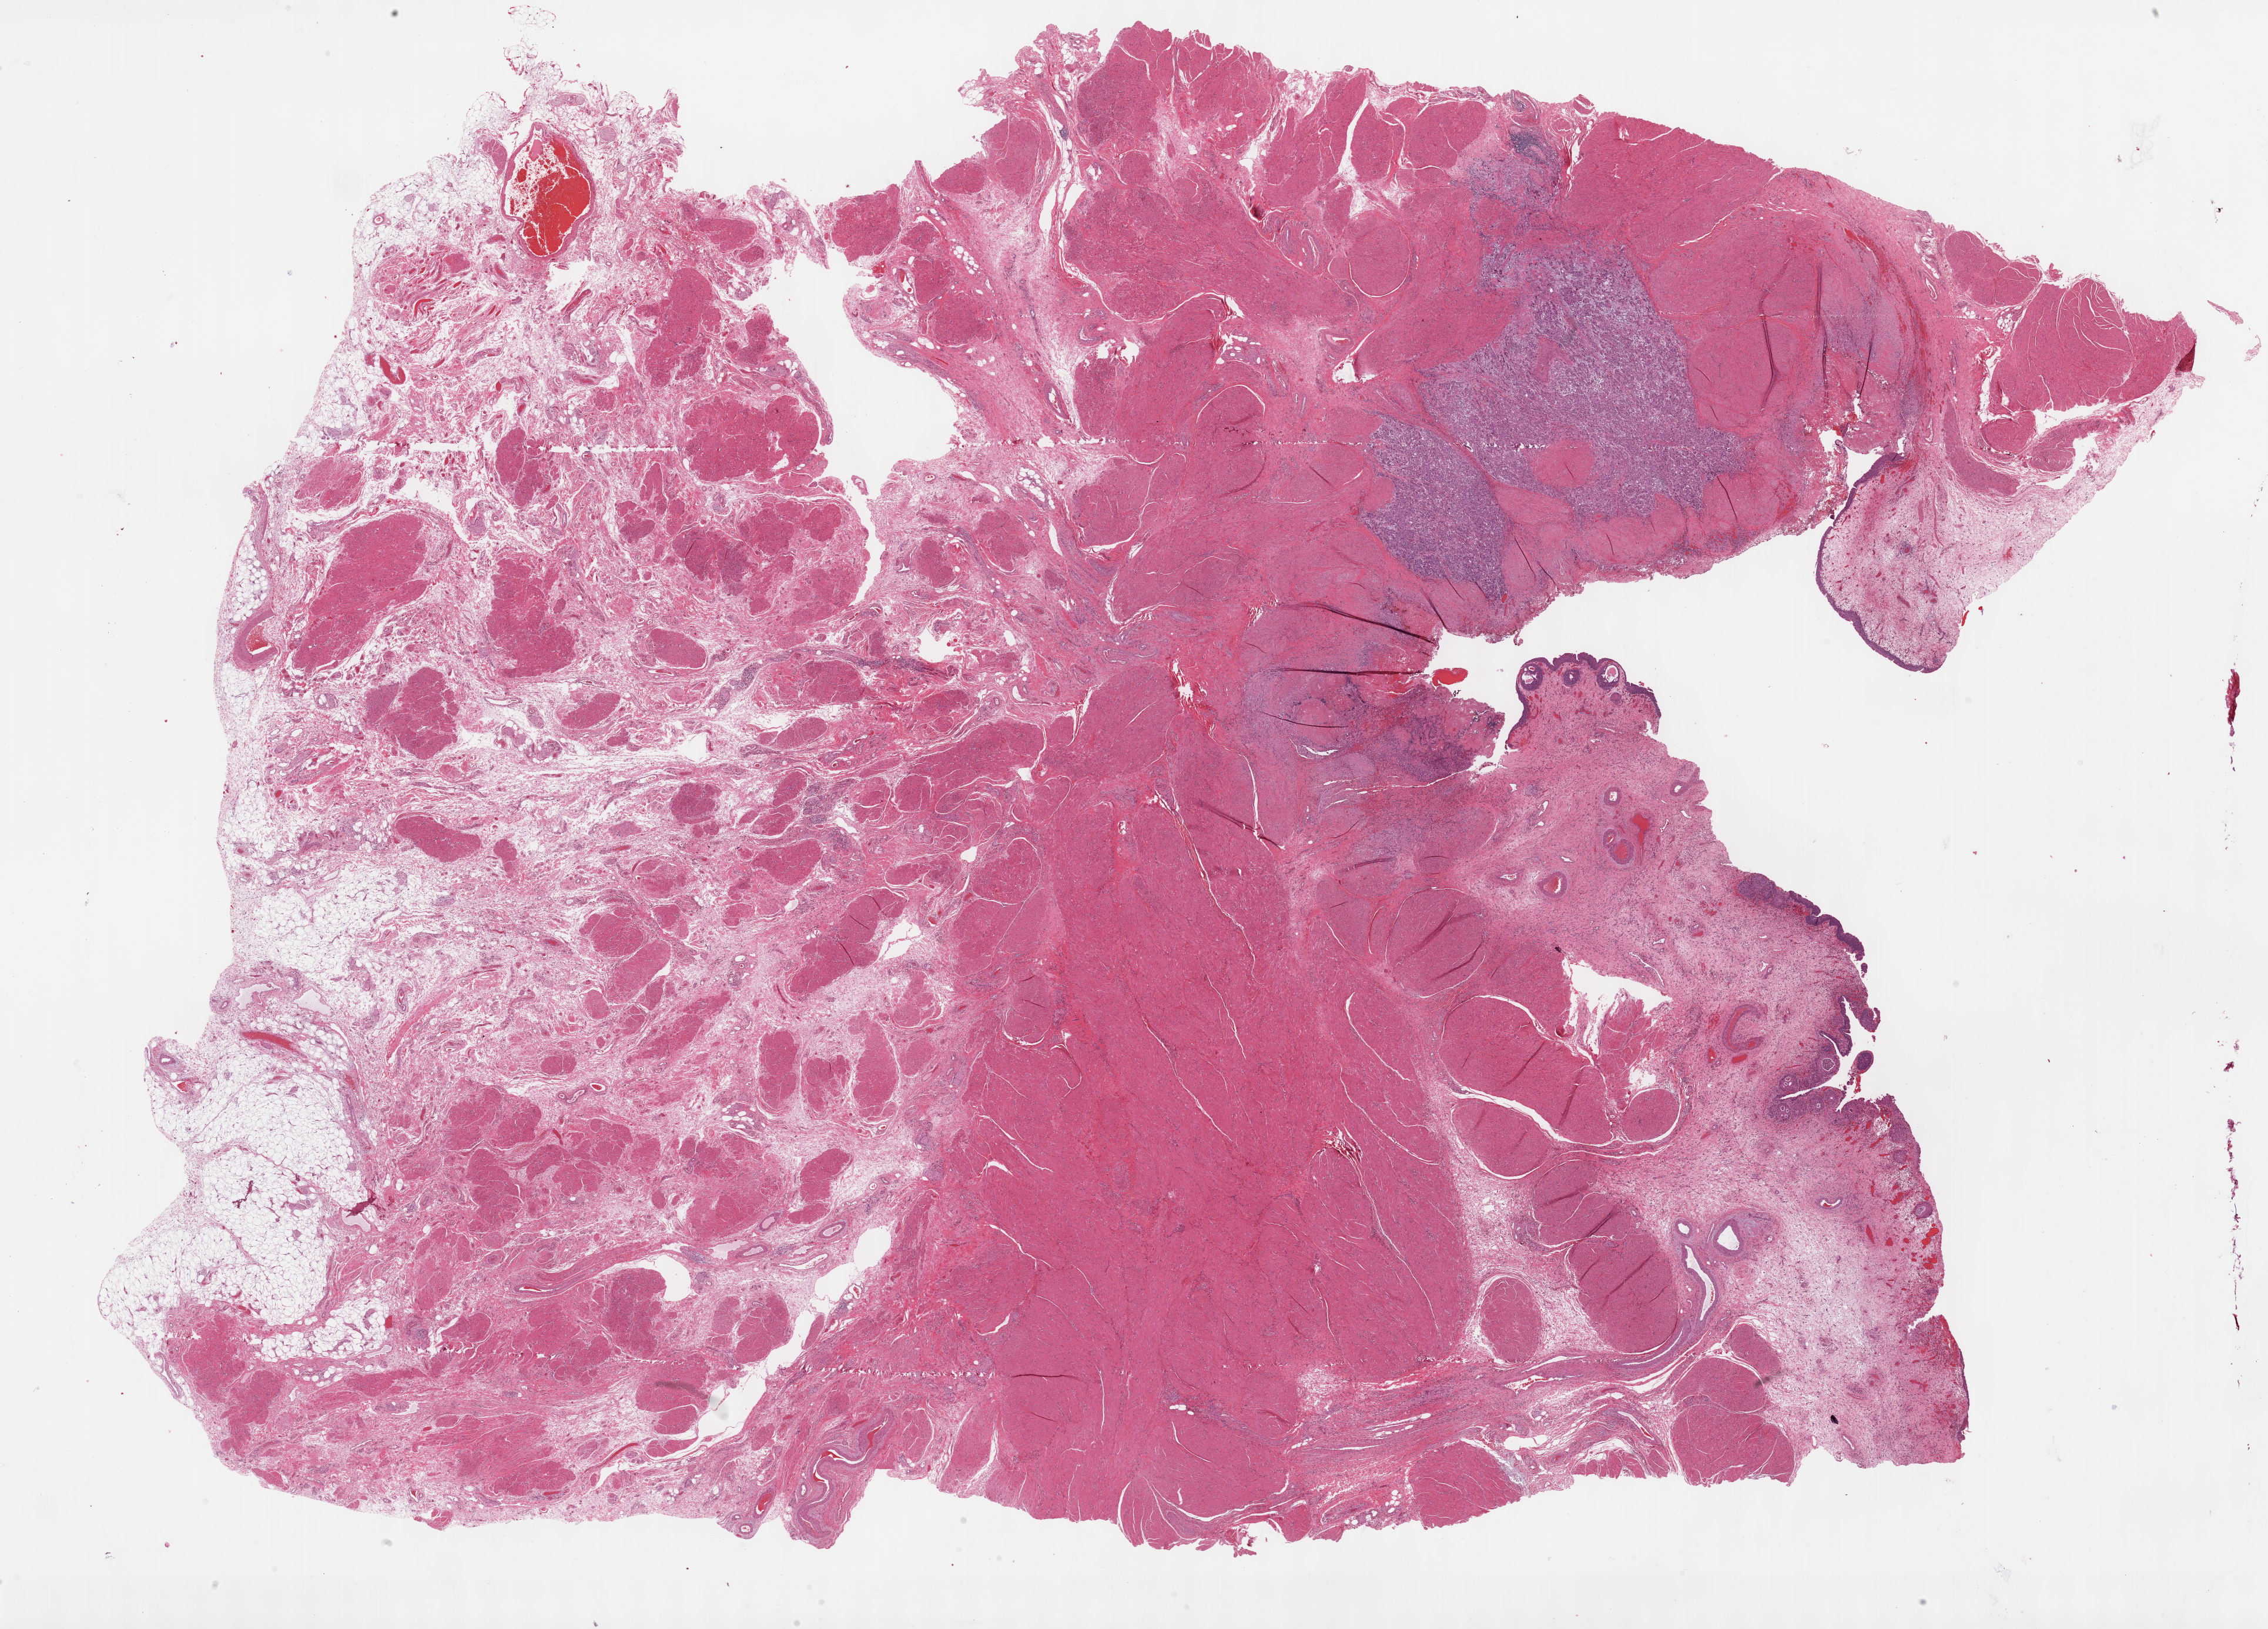
Hematoxylin and eosin (H&E) stained whole-slide image — a low-resolution overview of the entire scanned area, about 31.2 x 22.4 mm, FFPE section, sample: primary tumour, bladder. Male patient; age at initial diagnosis 76 years. Histologic grade: high grade.
TNM: T2b N0 MX. AJCC pathologic stage: II (7th edition). Histologic diagnosis: Transitional cell carcinoma (posterior wall of bladder).